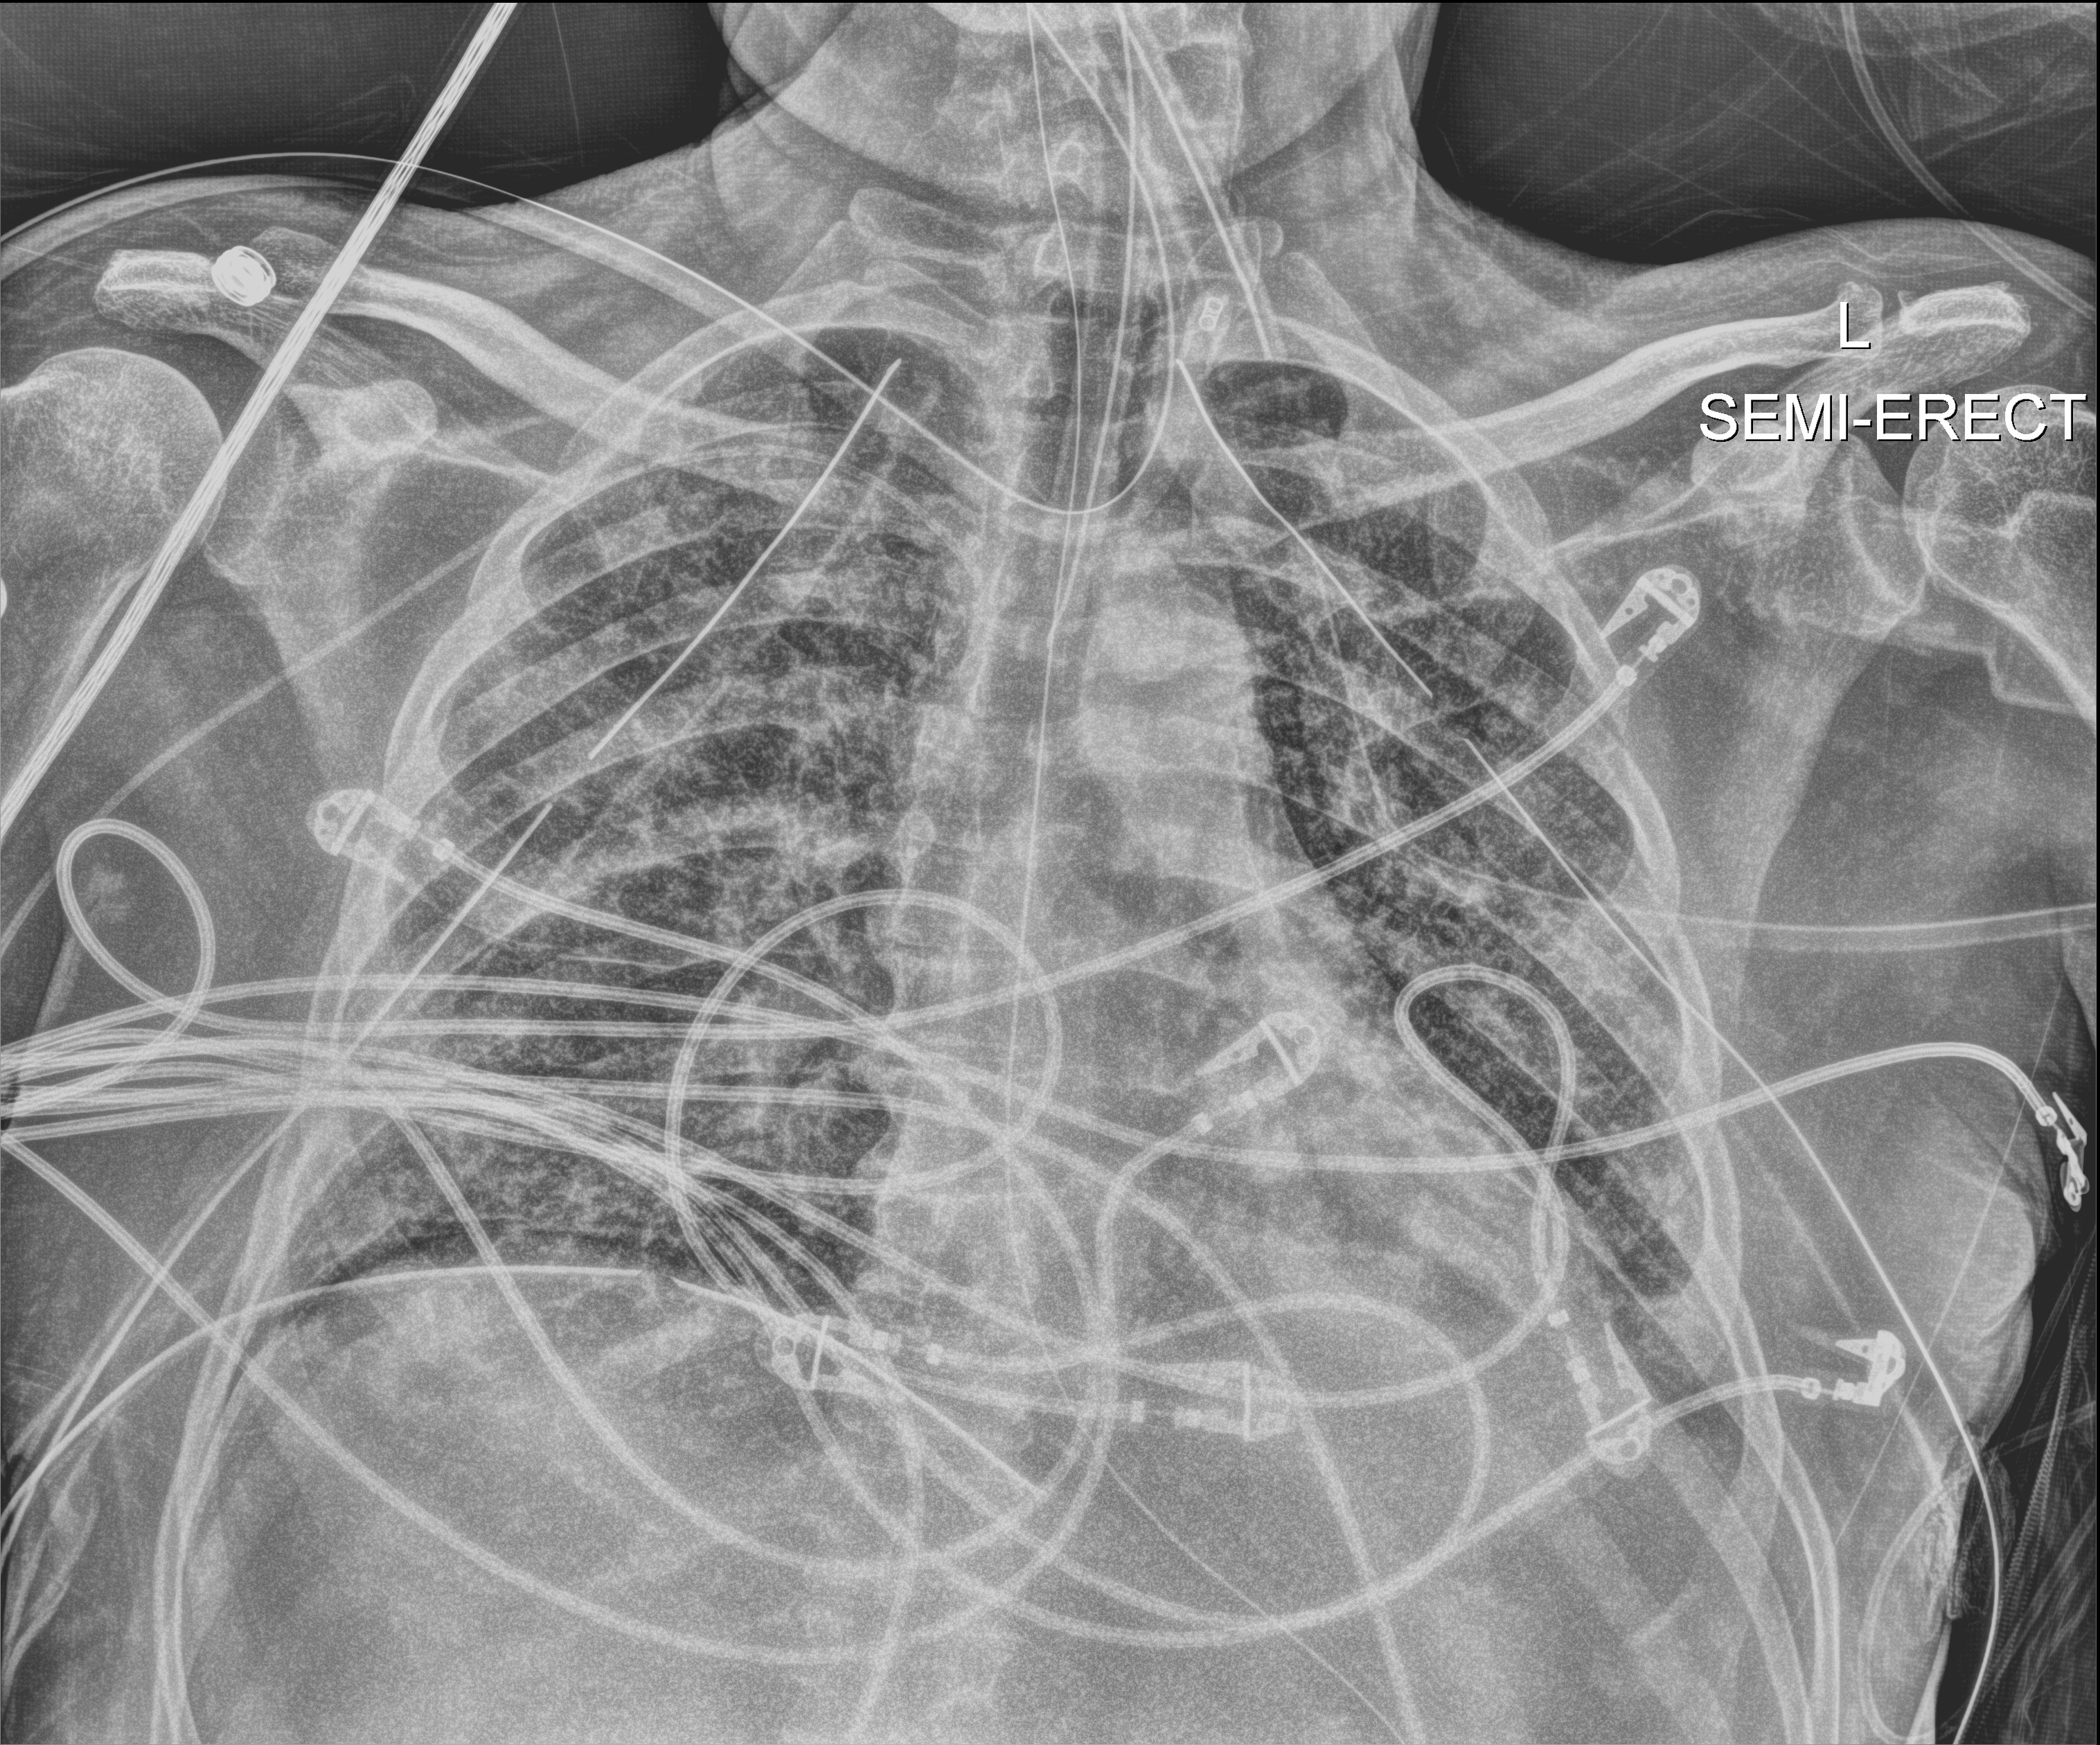
Portable chest radiograph; anteroposterior (AP) projection. Patient hospitalised with COVID-19; male, aged 18–59 years.
Hospital-stay facts (about this admission, not read from this image; timing relative to this image not recorded): COPD (admission record): no.